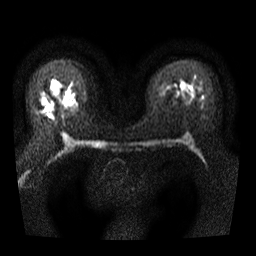
Breast MRI, one axial slice. Position 22 of 40 along the scan axis. Diffusion-weighted series; image 2 of 4 stored at this slice position (different b-values; order by instance number). 3 T. 5 mm slice thickness. 256 × 256 image matrix, field of view 300 × 300 mm. Female patient.
Structures marked on this image (expert manual segmentation):
- tumour on diffusion-weighted imaging: bounding box [x1, y1, x2, y2] px = [41, 99, 52, 112]